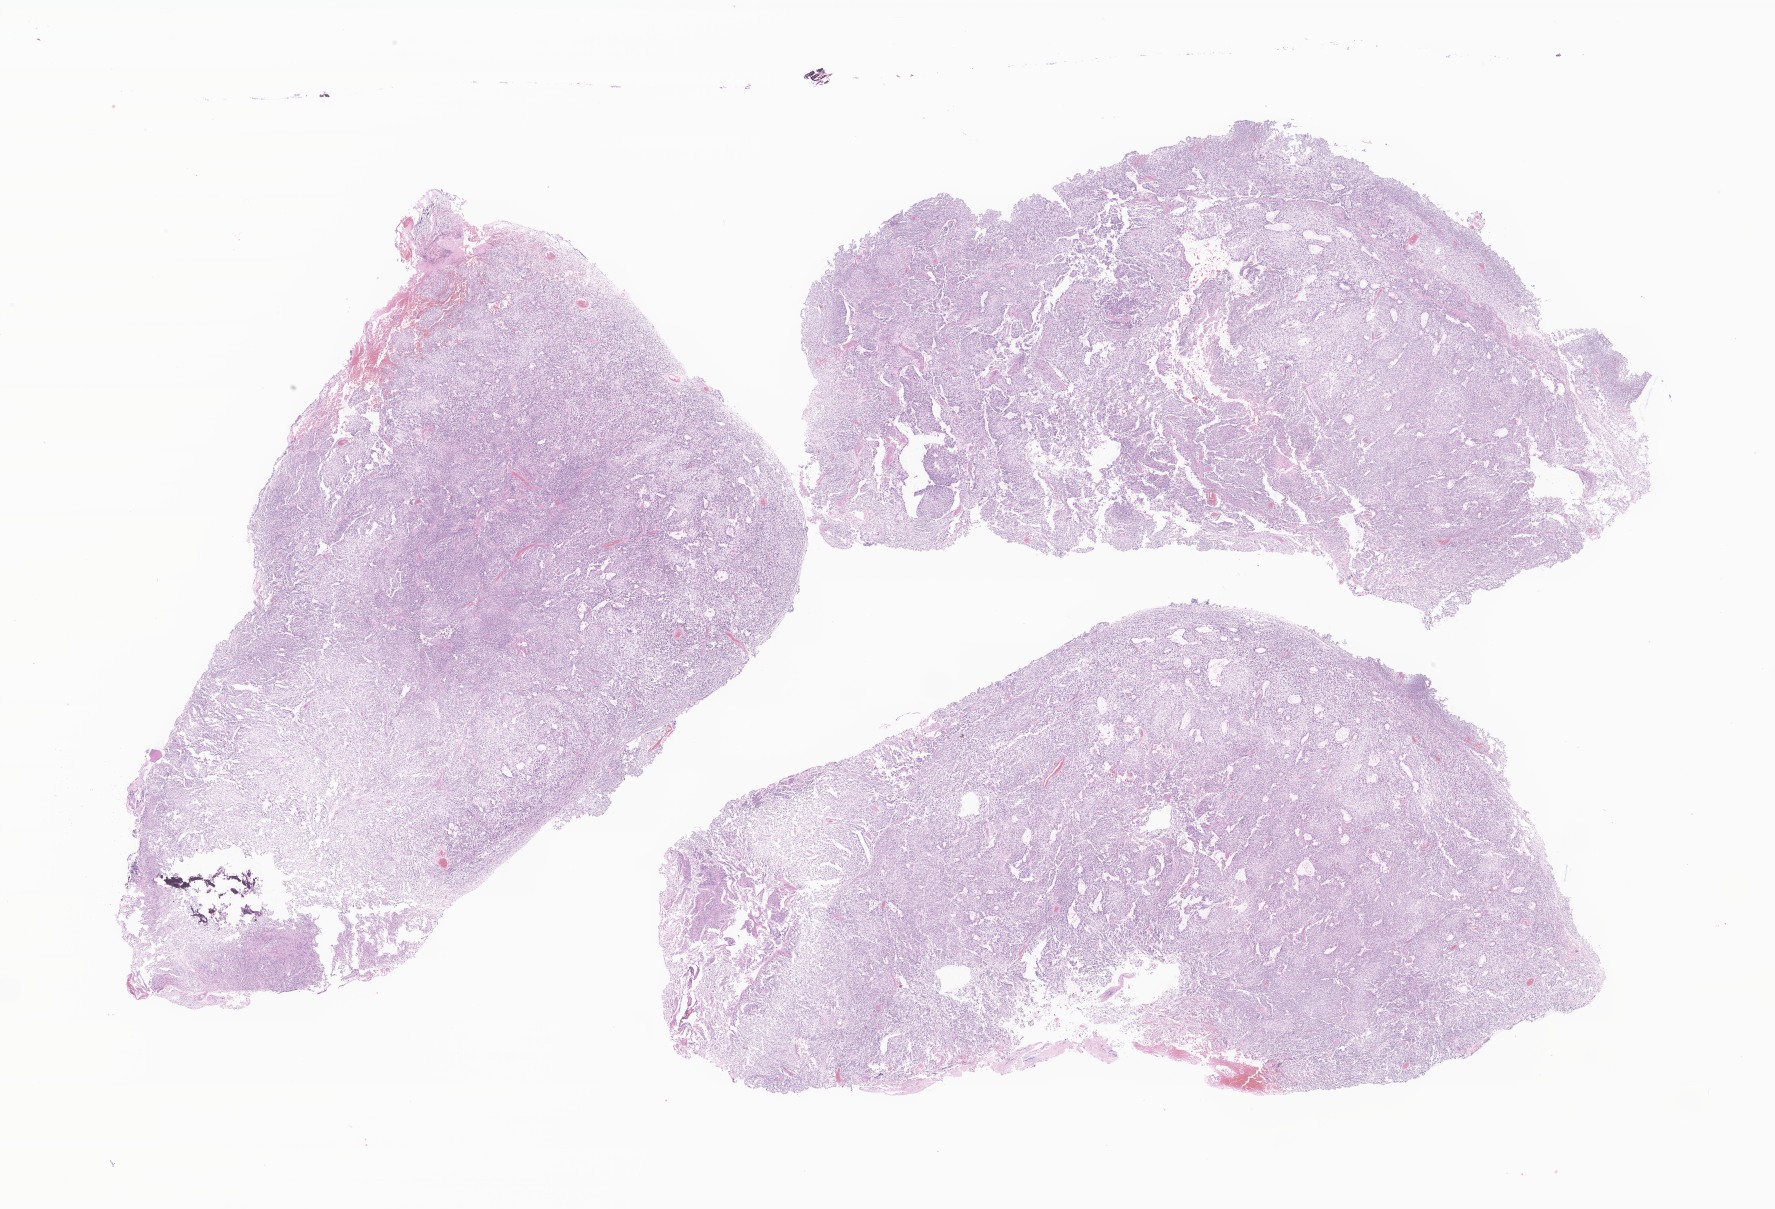
H&E whole-slide image of tumor tissue from the cerebellum, a low-resolution overview of the entire scanned area, about 29.9 x 20.4 mm, FFPE section. Male patient, age 84 months (7 years).
Diagnosis (ICD-O-3 morphology term): Medulloblastoma, NOS.